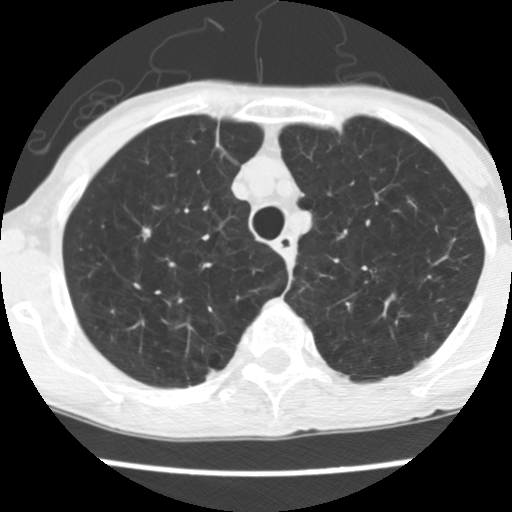
Low-dose screening chest CT, axial slice, baseline annual screen, lung window (W 1500 / L -600 HU), 2.5 mm slice thickness, slice 34 of 160 in the series, 512 × 512 image matrix, field of view 280 × 280 mm. Female, age 70 years at enrolment.
Expert reader's lesion annotation, box from (x=112, y=211) to (x=170, y=265) px. No non-calcified nodule or mass ≥4 mm was recorded by the screening reader at this exam. Later outcome: lung cancer diagnosed 226 days after this screen — large cell neuroendocrine carcinoma, right upper lobe, stage IA (AJCC 6th edition), 30 mm at pathology.